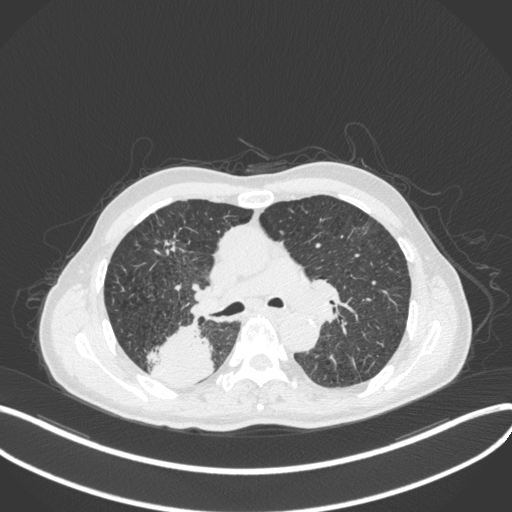
Chest CT, one axial slice. Slice 283 of 423 in the series (ordered by position). Reconstruction kernel B31f. Lung window (W 1500 / L -600 HU). 1 mm slice thickness. 512 × 512 image matrix, field of view 400 × 400 mm. Patient: male, 79 years. From the clinical record (not read from this slice): clinical TNM (as recorded): T3 N0 M0.
Outlined on this slice (rectangle marked by the reading radiologist):
- lung tumour (recorded histology: adenocarcinoma): bounding box <146,324,215,390> (left, top, right, bottom; pixels)